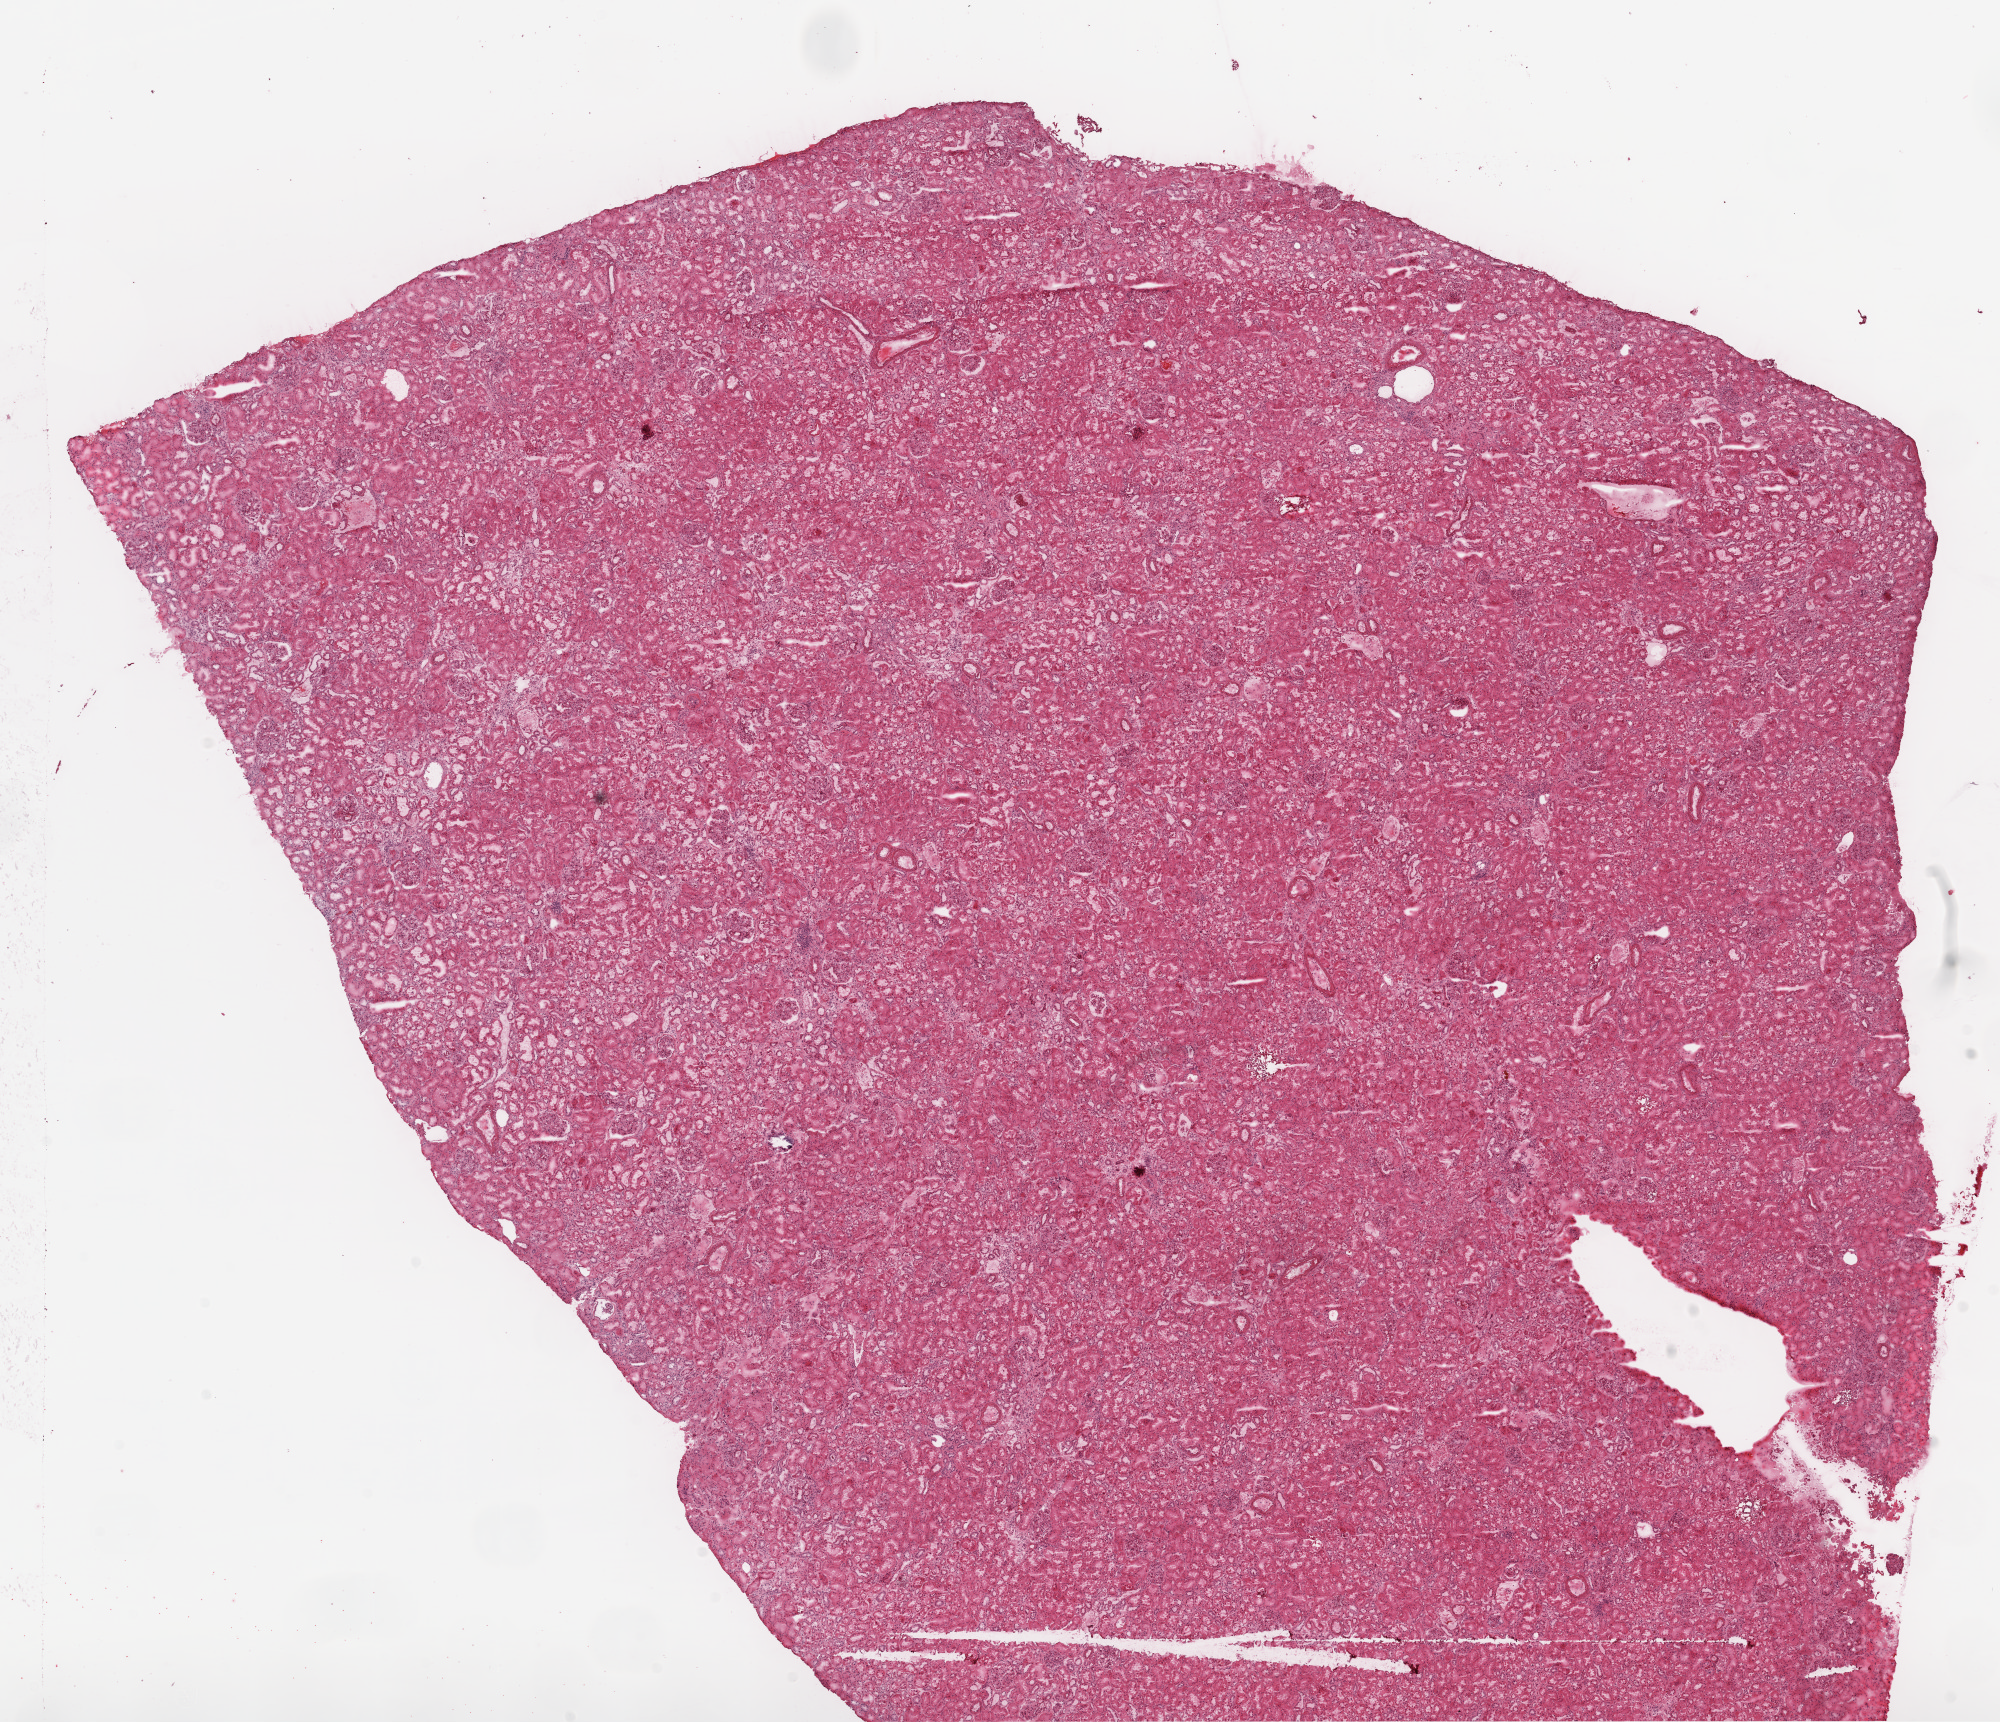
Digitized Hematoxylin and eosin (H&E) stained tissue section (whole slide), shown as a low-resolution overview of the whole scanned area (about 16.0 x 13.8 mm, from a 20x scan); frozen section from the top of the tissue portion; kidney, solid tissue normal (non-tumour tissue) sample. Female, age 75 years at initial diagnosis.
This section: solid tissue normal sample (biorepository sample class). Patient diagnosis: Clear cell adenocarcinoma, NOS.